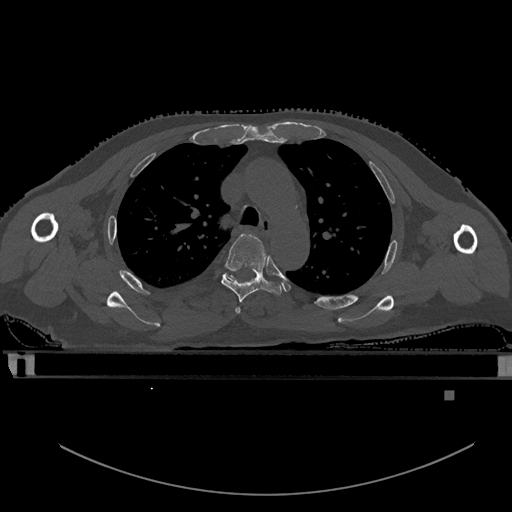
CT including the spine, one axial slice; slice 405 of 969 in the series (ordered by position); bone window (W 1800 / L 400 HU); 0.5 mm slice thickness; 512 × 512 image matrix, field of view 456 × 456 mm. Patient: male, 82 years. Case-level facts recorded for this patient, not image findings: primary cancer: prostate.
Outlined on this slice (semi-automatically segmented with operator editing):
- T3 vertebra: bounding box <235,307,241,314> (left, top, right, bottom; pixels)
- T4 vertebra: <221,233,282,303>
- T5 vertebra: <222,273,236,282>